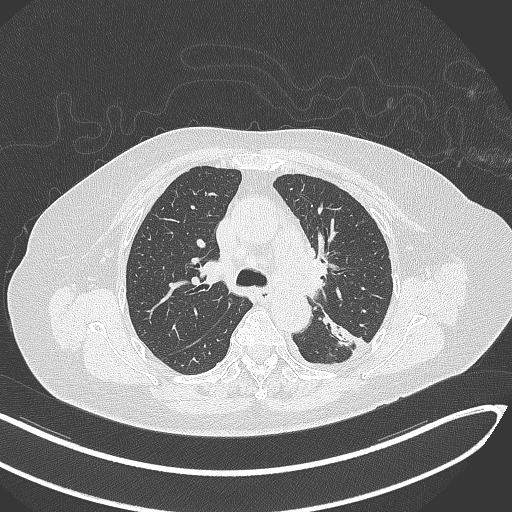
Chest CT, one axial slice. Position 209 of 270 along the scan axis. 120 kVp. Lung window (W 1500 / L -600 HU). 1 mm slice thickness. 512 × 512 image matrix. Patient: female, 76 years. From the clinical record (not read from this slice): clinical TNM (as recorded): T1c N0 M0.
Annotated regions visible in this slice (bounding box drawn by a radiologist):
- lung tumour (recorded histology: adenocarcinoma): box from (x=321, y=308) to (x=358, y=355) px